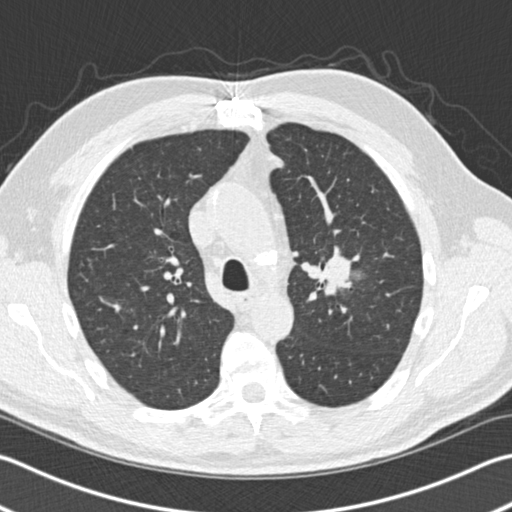
Chest CT (low-dose screening protocol), one axial image. Third annual screen. Lung window (W 1500 / L -600 HU). 2 mm slice thickness. Standard (soft-tissue) reconstruction kernel (B30f). Slice 48 of 153 in the series. 512 × 512 image matrix. Male participant, aged 65 years at enrolment.
Lesion marked by an expert reader, bounding box [x1, y1, x2, y2] px = [307, 239, 371, 303]. The screening reader recorded 4 non-calcified nodules or masses ≥4 mm on this exam; which of them this box marks is not recorded.